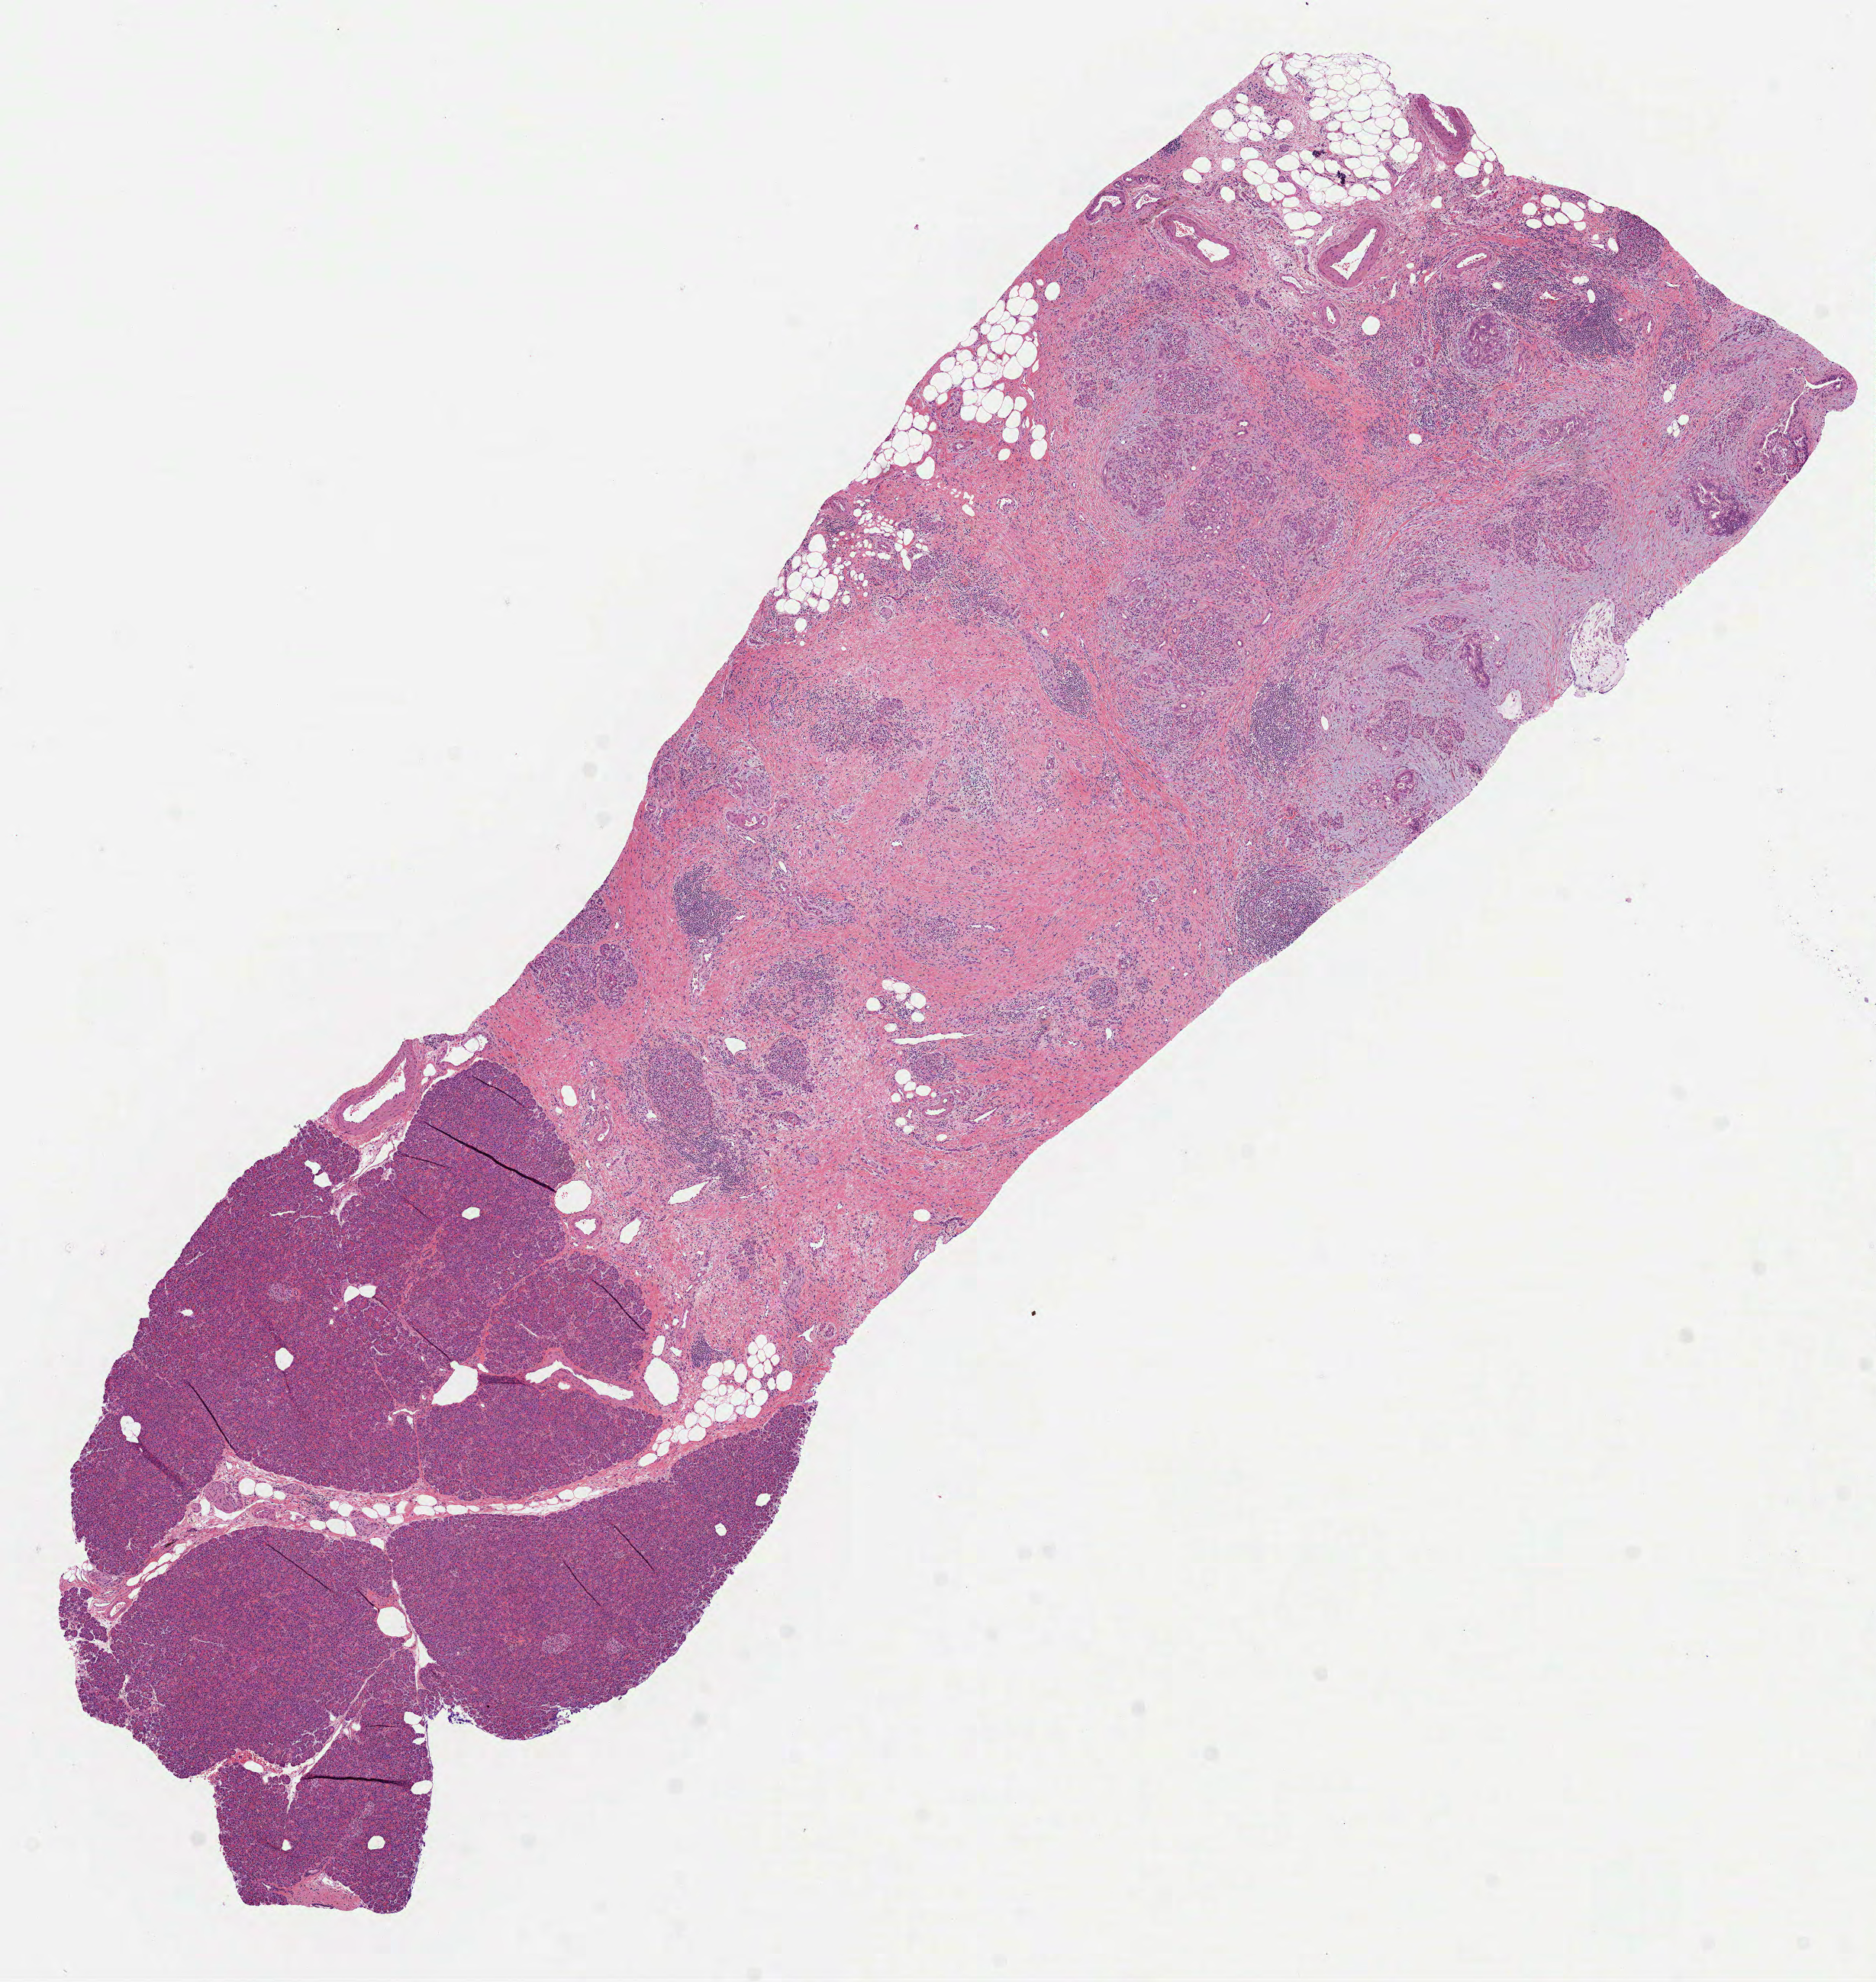
Whole-slide histology image, H&E-stained, shown as a low-resolution overview of the whole scanned area (about 9.9 x 10.5 mm, slide scanned at 40x); formalin-fixed paraffin-embedded (FFPE) diagnostic section; sample: primary tumour, pancreas. Patient: female, age at initial diagnosis 65 years. Histologic grade: G2 (moderately differentiated).
• histologic diagnosis: Infiltrating duct carcinoma, NOS (head of pancreas)
• AJCC pathologic stage: IIB (7th edition)